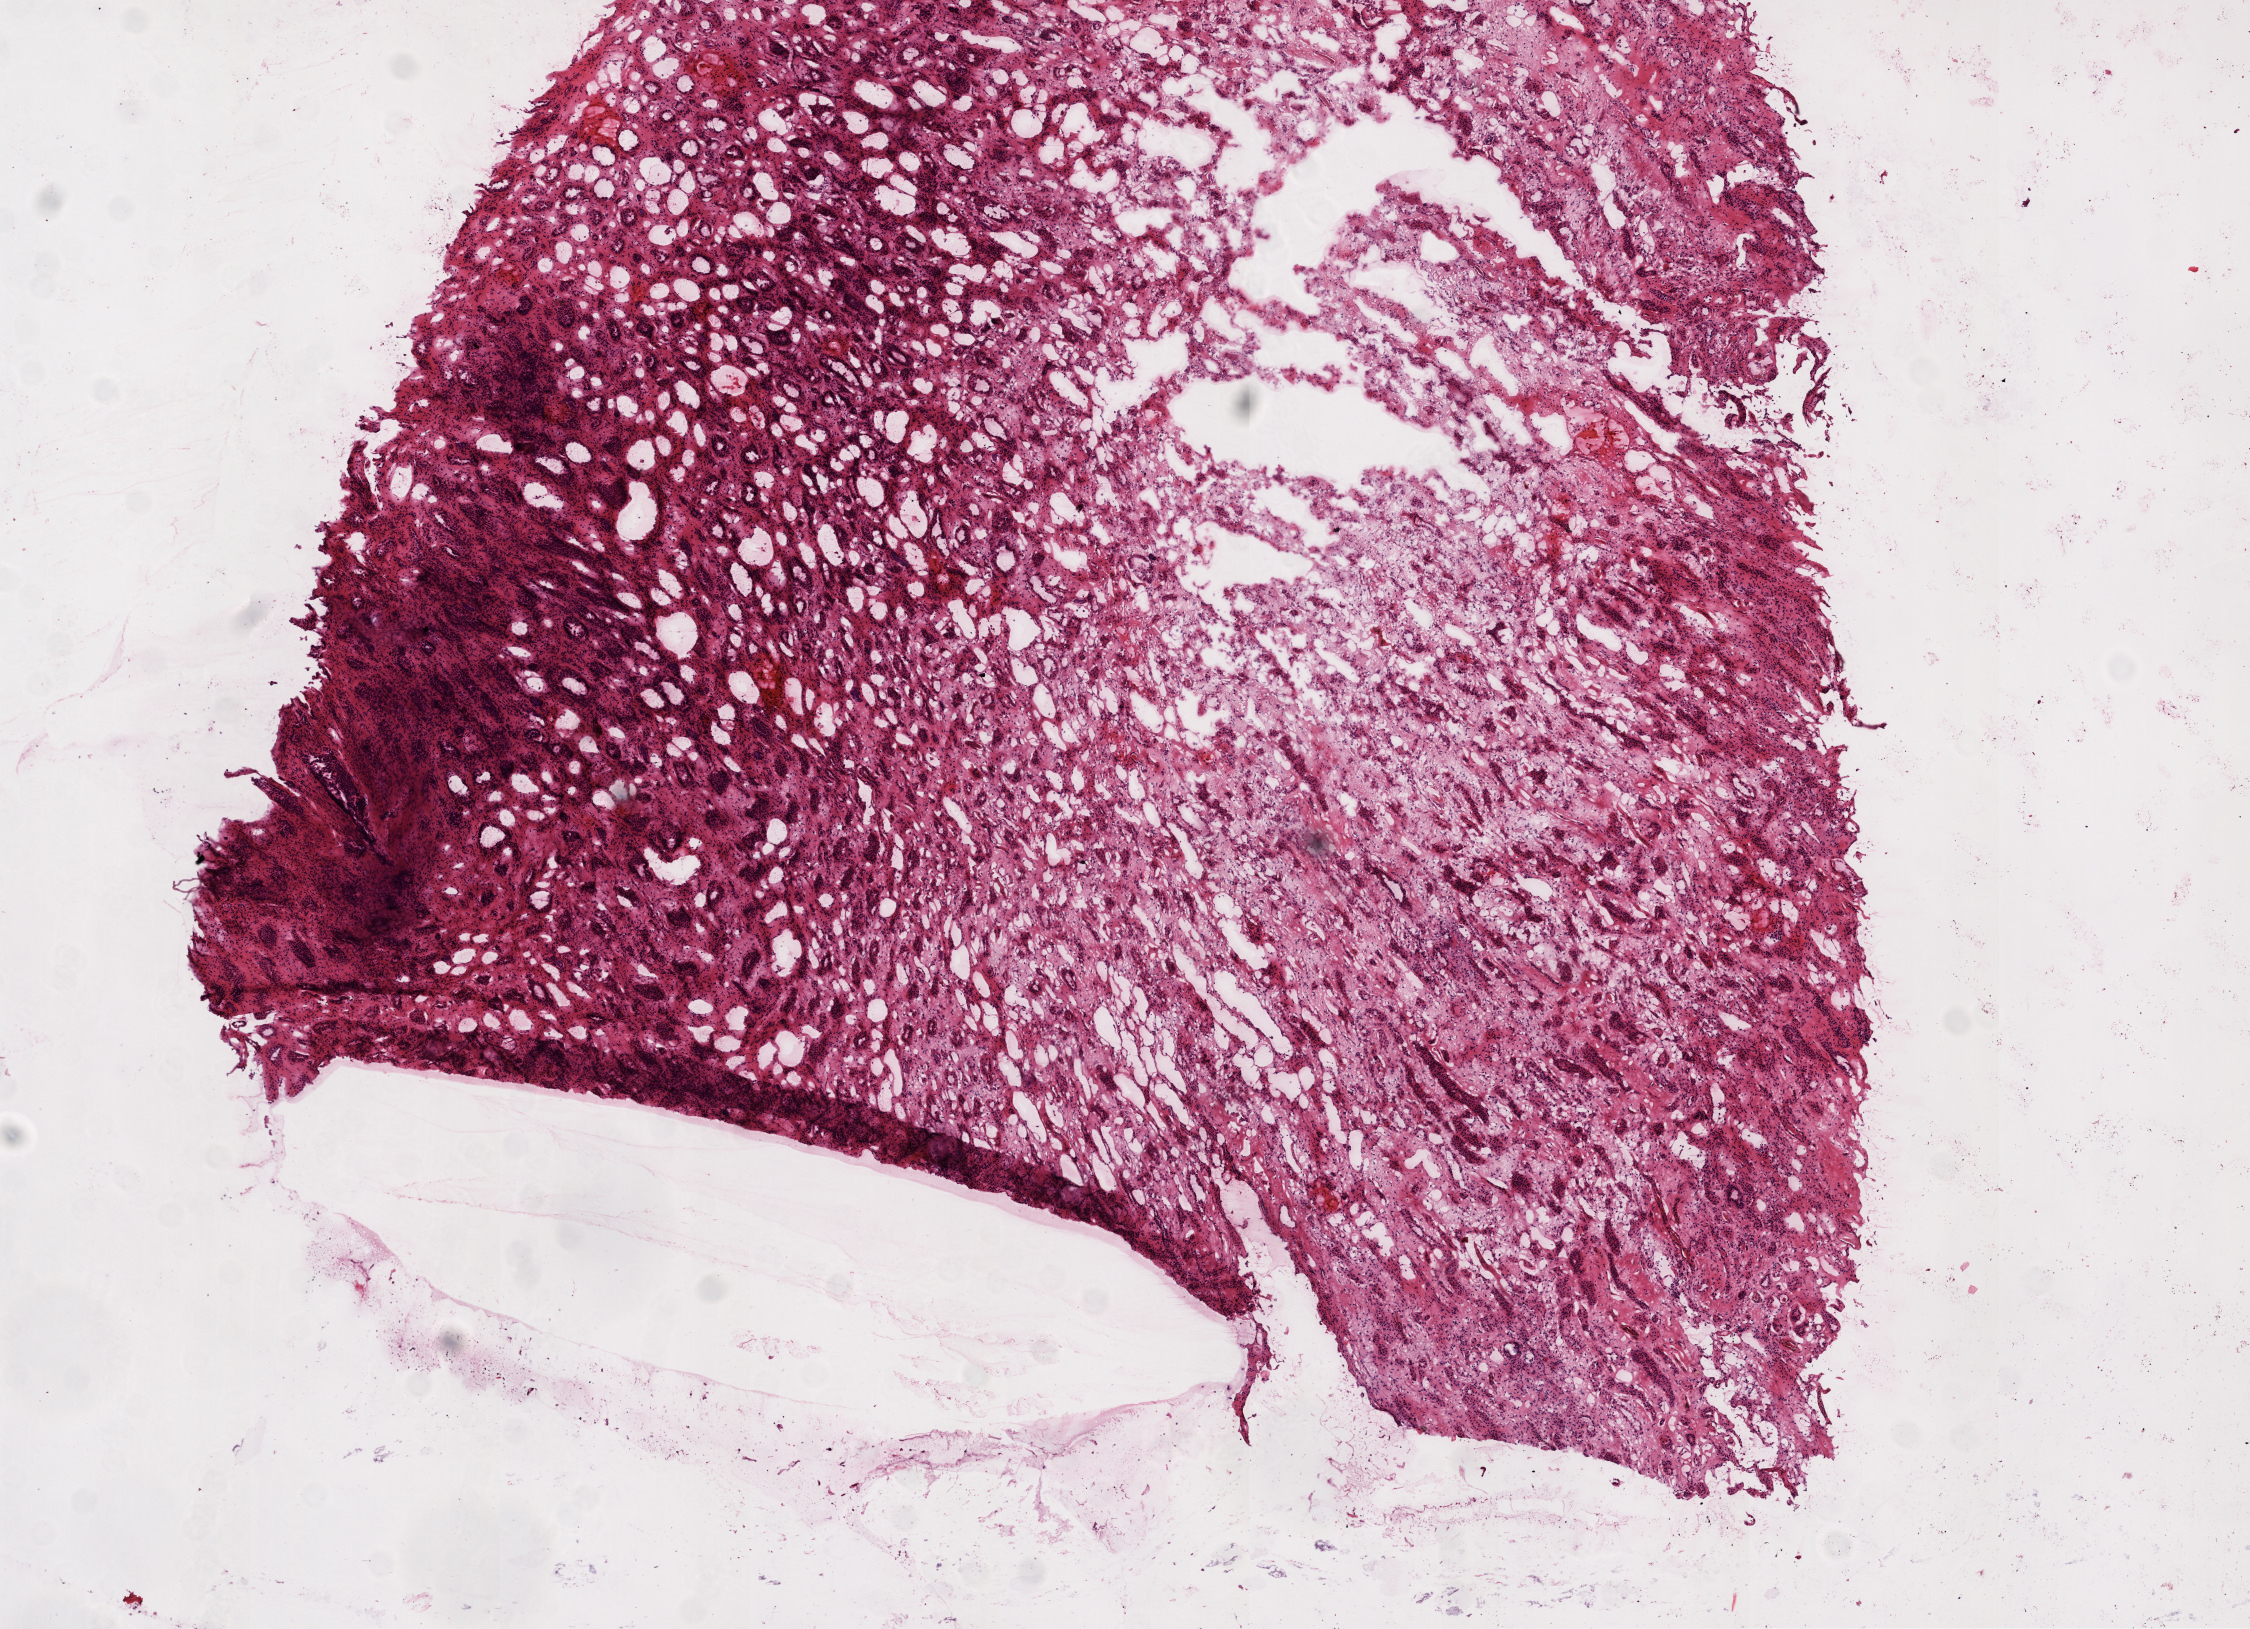
Whole-slide histology image, Hematoxylin and eosin (H&E) stained — low-resolution overview of the scanned area, about 9.0 x 6.5 mm (slide scanned at 20x). Frozen section from the top of the tissue portion. Solid tissue normal (non-tumour tissue) sample from the kidney. Patient: female, age at initial diagnosis 61 years.
This section: solid tissue normal sample (biorepository sample class). Patient diagnosis: Clear cell adenocarcinoma, NOS.